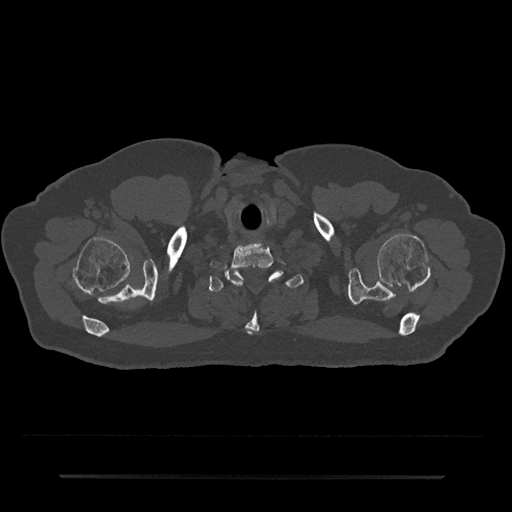
CT including the spine, one axial slice. Position 659 of 797 along the scan axis. Reconstruction kernel Br40s/3. Bone window (W 1800 / L 400 HU). 512 × 512 image matrix, field of view 437 × 437 mm. Male patient, age 69 years. From the clinical record (not read from this slice): primary cancer: prostate.
Annotated regions visible in this slice (semi-automatically segmented with operator editing):
- T1 vertebra: bounding box (x1, y1, x2, y2) in pixels: (209, 271, 304, 335)